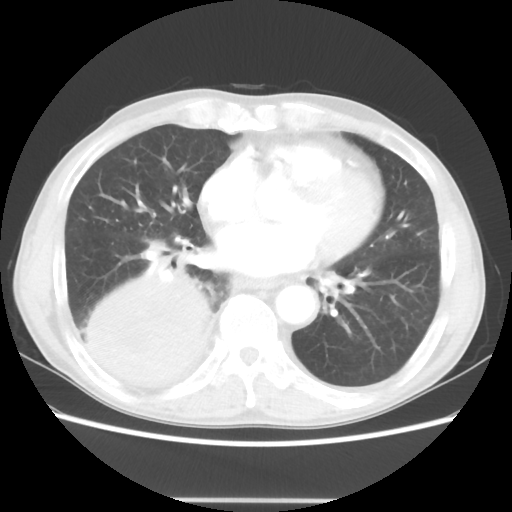
Chest CT, one axial slice; position 17 of 48 along the scan axis; reconstruction kernel STANDARD; 100 kVp; lung window (W 1500 / L -600 HU); 512 × 512 image matrix. Male patient, age 66 years. From the clinical record (not read from this slice): clinical TNM (as recorded): T4 N1 M1.
Outlined on this slice (rectangle marked by the reading radiologist):
- lung tumour (recorded histology: small cell carcinoma): bounding box <66,259,222,403> (left, top, right, bottom; pixels)